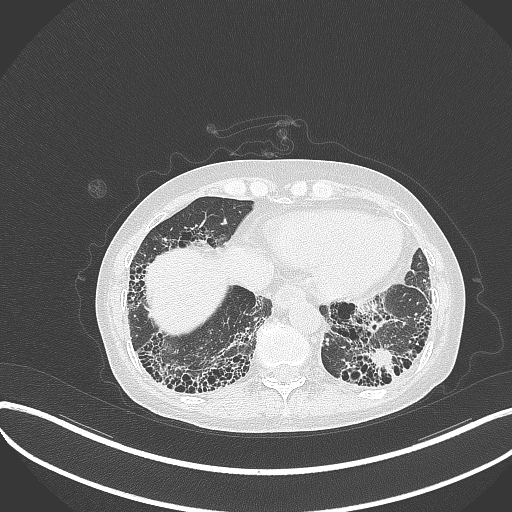
Chest CT, one axial slice. Slice 68 of 373 in the series (ordered by position). 120 kVp. Lung window (W 1500 / L -600 HU). 1 mm slice thickness. 512 × 512 image matrix. Female patient, age 56 years. Case-level facts recorded for this patient, not image findings: clinical TNM (as recorded): T1 N0 M0.
Outlined on this slice (bounding box drawn by a radiologist):
- lung tumour (recorded histology: adenocarcinoma): bounding box <372,345,398,371> (left, top, right, bottom; pixels)